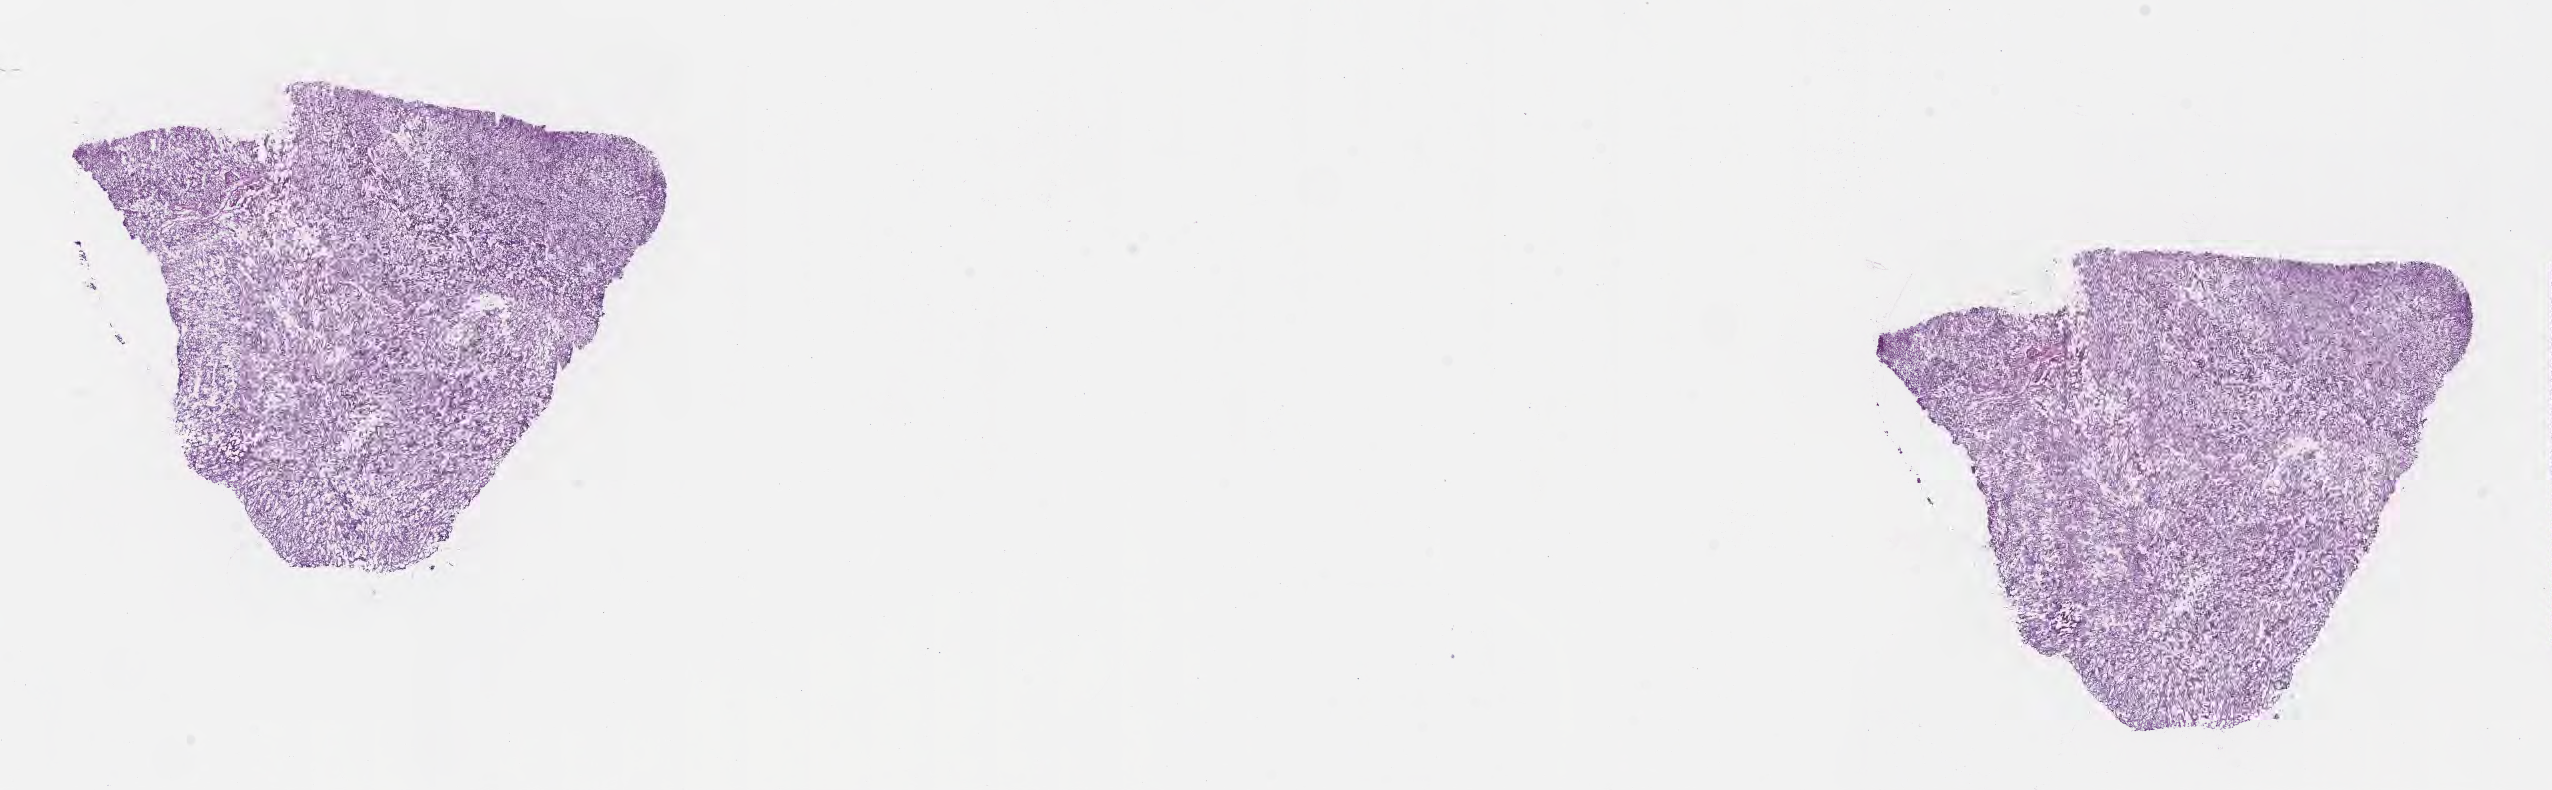
Haematoxylin and eosin whole-slide image, whole scanned area (about 20.6 x 6.4 mm) shown as a low-resolution overview. Cryosection. Recurrent tumor. Site: brain. Patient: female, age at initial diagnosis 53 years. Composition of this section per pathologist review: tumor cells 72%, tumor nuclei 89%, stromal cells 14%, necrosis 5%, normal cells 9%. Infiltration values recorded for this section: lymphocyte infiltration 0%, monocyte infiltration 0%, neutrophil infiltration 0%.
Patient diagnosis: Glioblastoma, NOS. Section: bottom of the tissue portion.